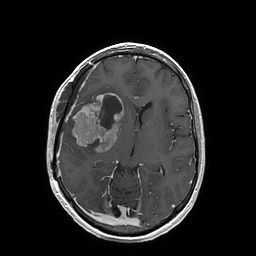
Brain MRI from a brain-tumour surgery series, one axial slice. Position 91 of 202 along the scan axis. T1-weighted post-contrast. 1 mm slice thickness. 256 × 256 image matrix, field of view 250 × 250 mm. Case-level facts recorded for this patient, not image findings: histopathology: Glioblastoma; WHO grade: 4; IDH mutation: no; tumour location: Right Insular.
Annotated regions visible in this slice (expert manual segmentation):
- tumour: box from (x=73, y=93) to (x=123, y=152) px